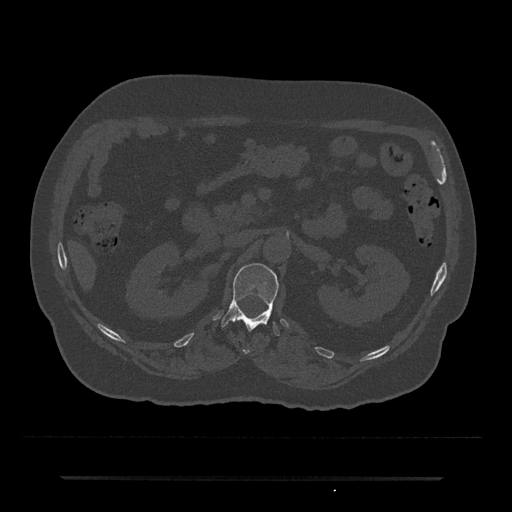
CT including the spine, one axial slice; slice 74 of 797 in the series (ordered by position); 120 kVp; bone window (W 1800 / L 400 HU); 512 × 512 image matrix. Male patient, age 69 years. Case-level facts recorded for this patient, not image findings: primary cancer: prostate.
Structures marked on this image (semi-automatic segmentation, software-assisted and operator-edited):
- L1 vertebra: box from (x=221, y=263) to (x=279, y=336) px
- T12 vertebra: (x=242, y=349)–(x=250, y=354)